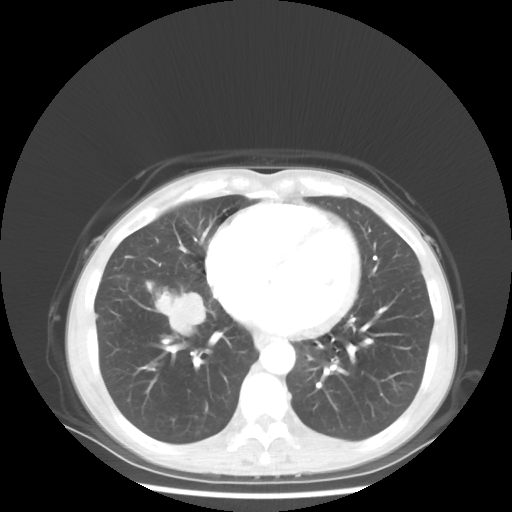
Chest CT, one axial slice. Slice 21 of 56 in the series (ordered by position). 80 kVp. Lung window (W 1500 / L -600 HU). 5 mm slice thickness. 512 × 512 image matrix, field of view 360 × 360 mm. Patient: female, 57 years. From the clinical record (not read from this slice): clinical TNM (as recorded): T1c N3 M1a; histopathological grade: G3.
Structures marked on this image (bounding box drawn by a radiologist):
- lung tumour (recorded histology: adenocarcinoma): bounding box [x1, y1, x2, y2] px = [152, 289, 211, 334]